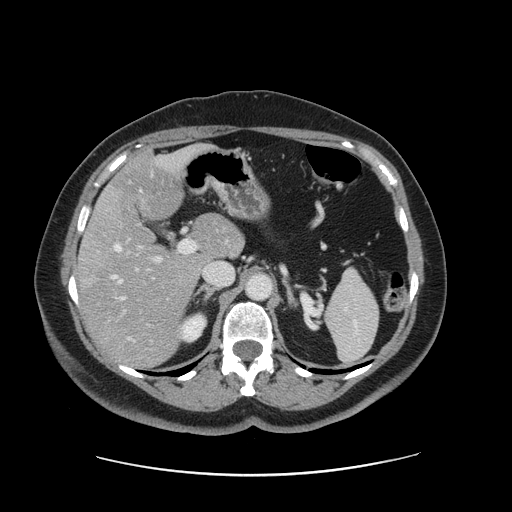
Contrast-enhanced abdominal CT, one axial slice. Position 87 of 161 along the scan axis. 120 kVp. Intravenous contrast given. Soft-tissue window (W 400 / L 40 HU). 512 × 512 image matrix, field of view 398 × 398 mm. Female patient, age 62 years. Case-level facts recorded for this patient, not image findings: diagnosis: colorectal cancer liver metastases, imaged before liver resection; multiple liver metastases: no; largest metastasis: 2.5 cm; chemotherapy before resection: yes.
Annotated regions visible in this slice (expert manual segmentation):
- hepatic veins: bounding box [x1, y1, x2, y2] px = [113, 190, 142, 283]
- liver: [80, 147, 242, 368]
- planned liver remnant (the part of the liver to remain after resection): [109, 147, 242, 263]
- portal vein (with intrahepatic branches): [115, 240, 196, 326]